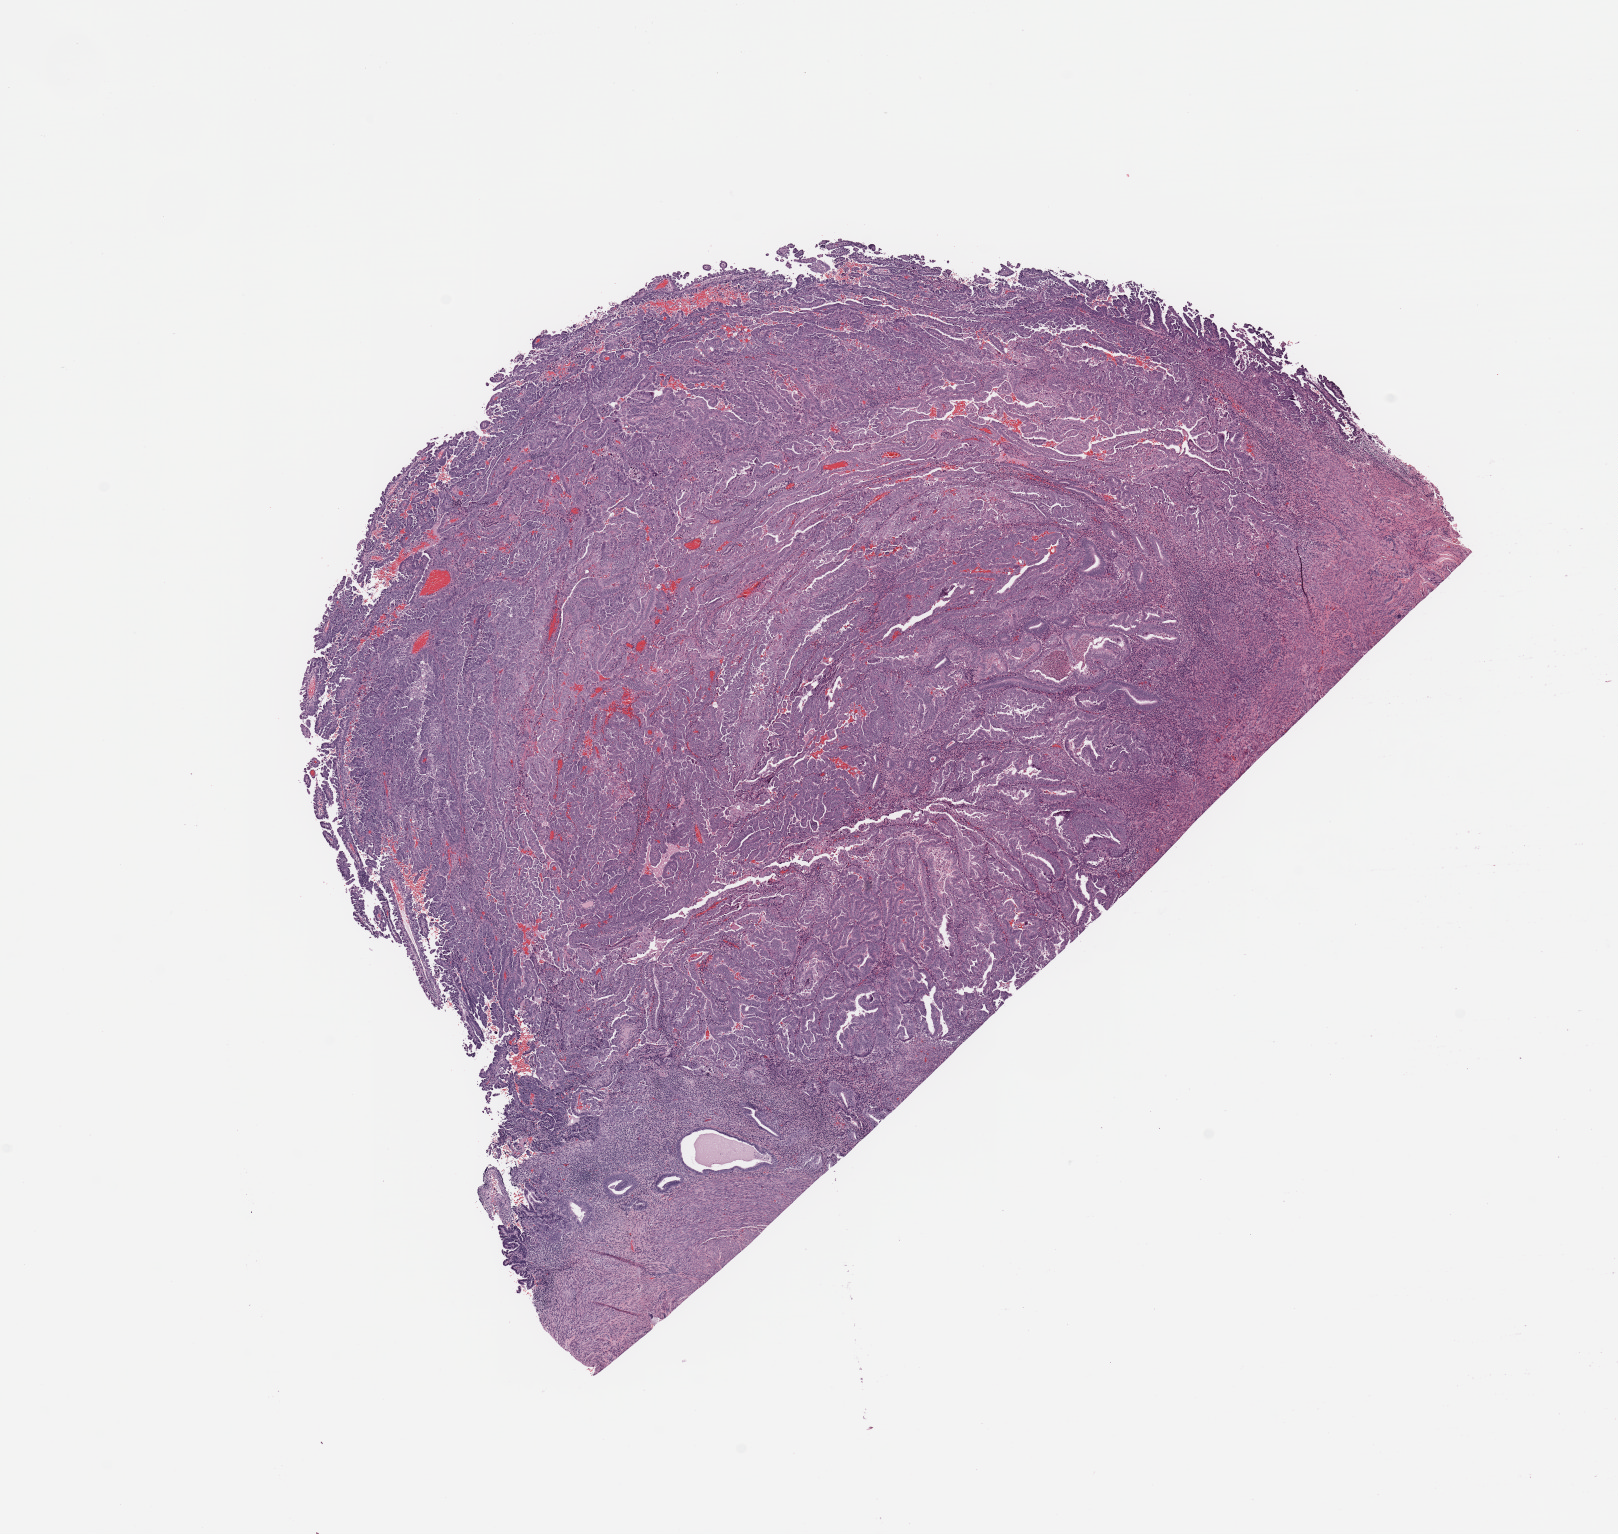
Digitized H&E-stained tissue section (whole slide), shown as a low-resolution overview of the whole scanned area (about 12.8 x 12.1 mm); tumour tissue sample, sampled site: uterus. 63-year-old female patient. Histologic grade: G3 (poorly differentiated). Slide review estimates, as recorded: tumour nuclei 90%, necrosis 0%.
Diagnosis: Endometrioid adenocarcinoma, NOS. AJCC pathologic stage: III.